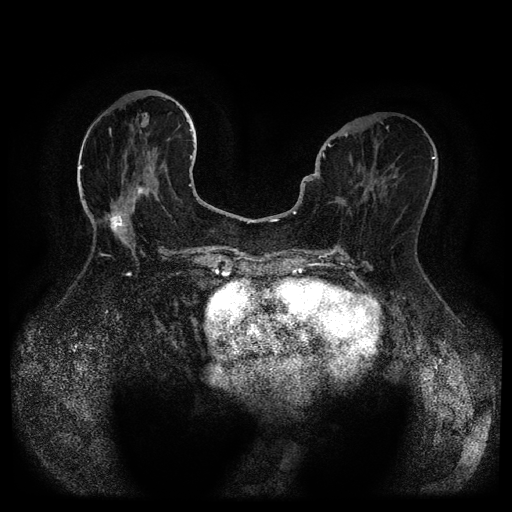
Breast MRI (dynamic contrast-enhanced, multi-phase), one axial slice; slice 41 of 116 in the series (ordered by position); dynamic contrast-enhanced series, time point 2 of 5 at this slice position (early post-contrast); 1.5 T; TE 2.6 ms, TR 5.3 ms; 512 × 512 image matrix, field of view 350 × 350 mm. Female patient, age 75 years.
Structures marked on this image (semi-automatic segmentation, software-assisted and operator-edited):
- breast lesion (labelled benign in the annotation): bounding box [x1, y1, x2, y2] px = [136, 186, 149, 197]
- breast lesion (labelled benign in the annotation): [106, 212, 125, 235]